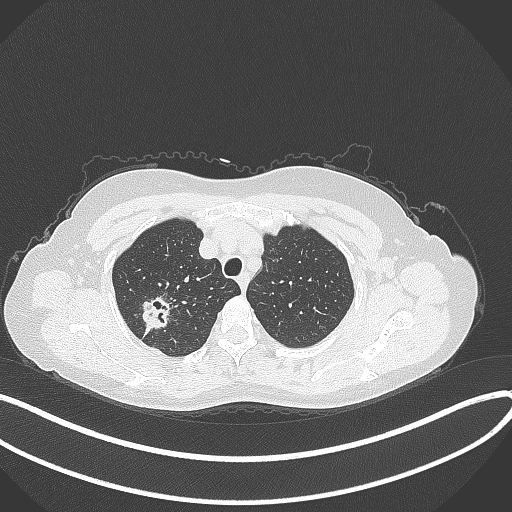
Chest CT, one axial slice; position 298 of 337 along the scan axis; 120 kVp; lung window (W 1500 / L -600 HU); 512 × 512 image matrix, field of view 400 × 400 mm. Patient: female, 50 years. From the clinical record (not read from this slice): clinical TNM (as recorded): T1c N0 M0.
Outlined on this slice (rectangle marked by the reading radiologist):
- lung tumour (recorded histology: adenocarcinoma): box from (x=133, y=294) to (x=174, y=333) px